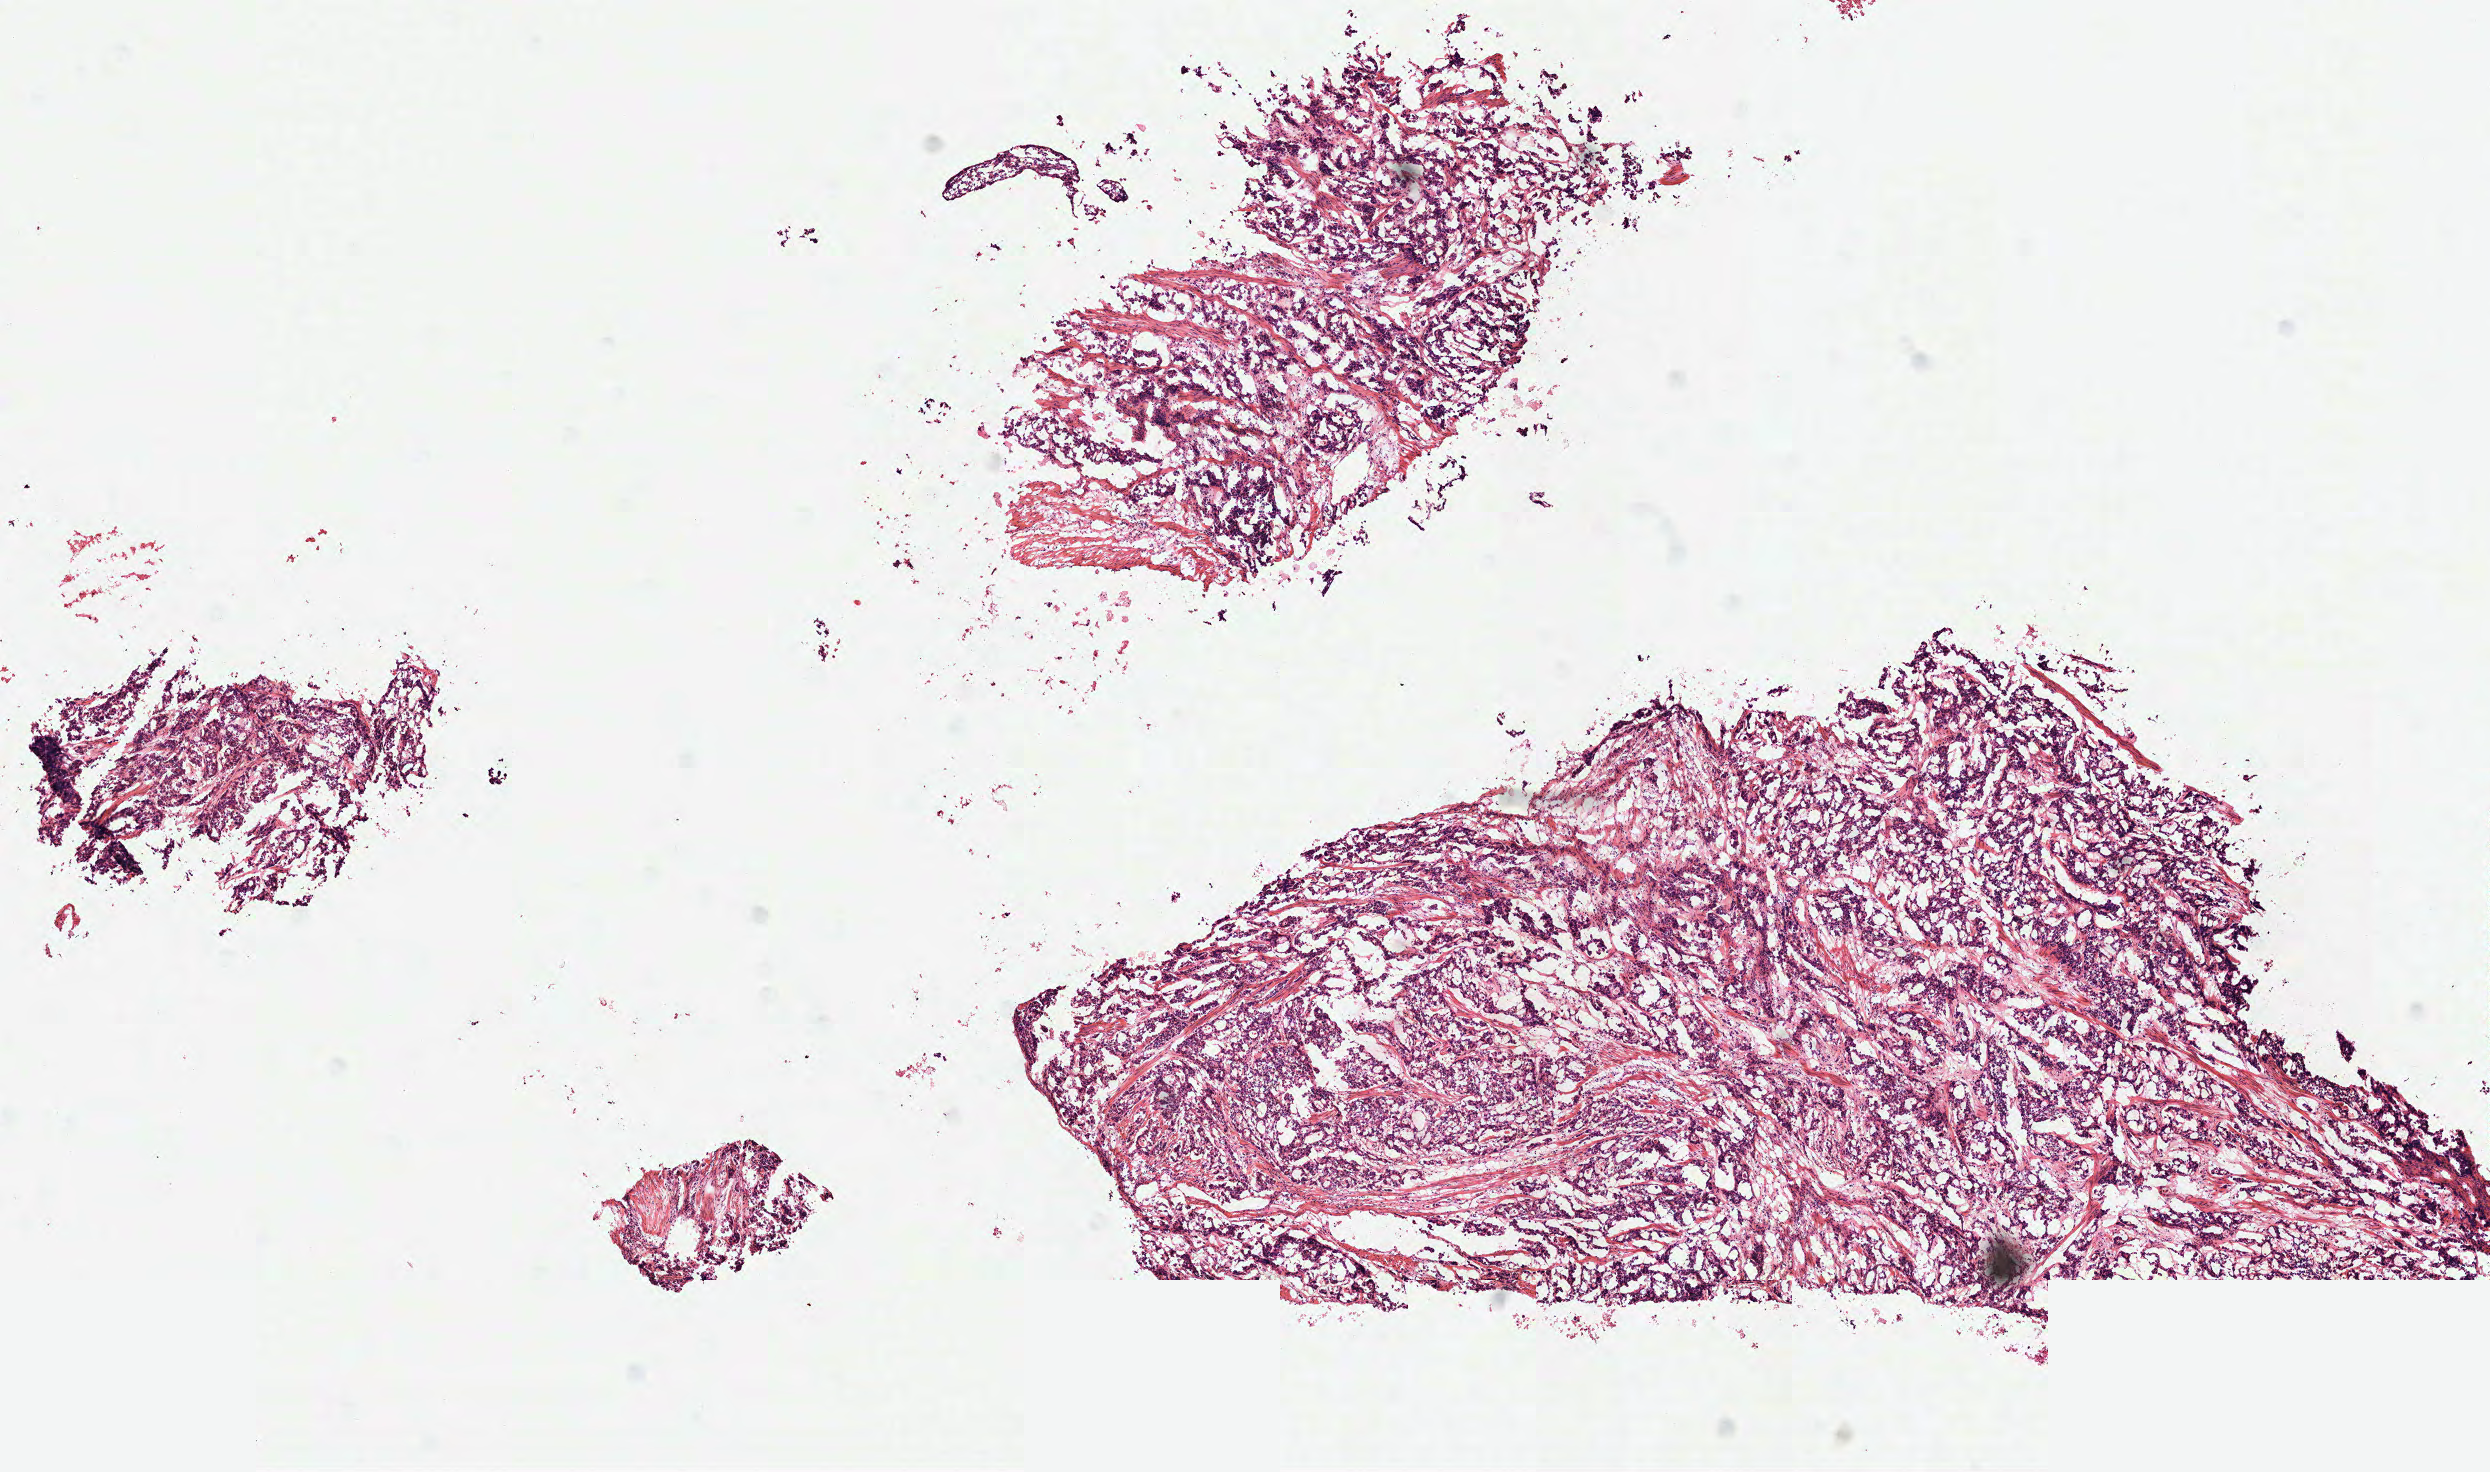
Digitized H&E tissue section (whole slide) — whole scanned area (about 10.0 x 5.9 mm, from a 40x scan) shown as a low-resolution overview, frozen section, primary tumour sample from the stomach. Female patient; age at initial diagnosis 72 years. Histologic grade: G2 (moderately differentiated). Slide review estimates, as recorded: tumour cells 90%, tumour nuclei 85%, normal cells 0%, stromal cells 10%, necrosis 0%.
Diagnosis: Adenocarcinoma, intestinal type (gastric antrum). AJCC pathologic stage: II (6th edition).